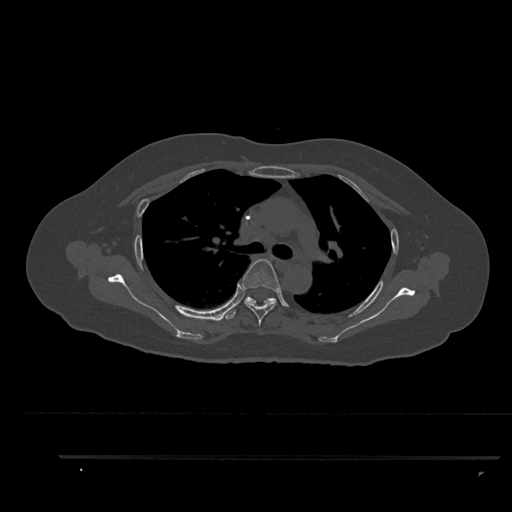
CT including the spine, one axial slice. Reconstruction kernel Br40s/3. 120 kVp. Bone window (W 1800 / L 400 HU). 0.5 mm slice thickness. 512 × 512 image matrix, field of view 408 × 408 mm. Female patient, age 44 years. From the clinical record (not read from this slice): primary cancer: renal; vertebrae with lytic lesions (as recorded): L1.
Structures marked on this image (semi-automatic segmentation, software-assisted and operator-edited):
- T4 vertebra: bounding box <241,259,280,326> (left, top, right, bottom; pixels)
- T5 vertebra: <225,296,275,320>